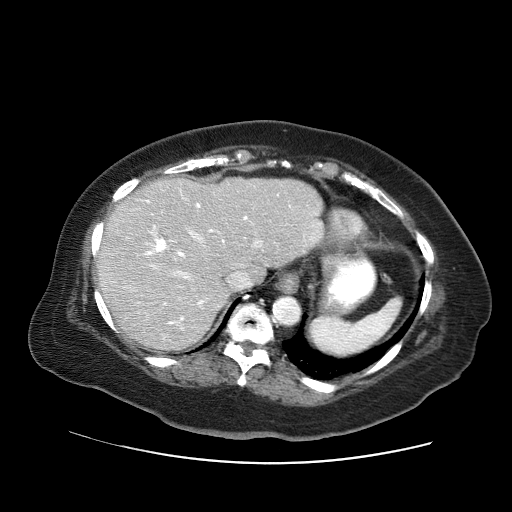
Contrast-enhanced abdominal CT (liver protocol), one axial slice. Position 46 of 71 along the scan axis. Reconstruction kernel STANDARD. Soft-tissue window (W 400 / L 40 HU). 2.5 mm slice thickness. 512 × 512 image matrix. From the clinical record (not read from this slice): diagnosis: hepatocellular carcinoma (patient treated with transarterial chemoembolisation; whether this scan precedes or follows treatment is not stated here); TNM stage (as recorded): Stage-II; Child-Pugh class: A; tumour differentiation: poorly differentiated; tumour nodularity: multinodular.
Structures marked on this image (semi-automatically segmented with operator editing):
- liver parenchyma outside the tumour (the mass and vessels are separate outlines, so this box may not span the whole liver): box from (x=96, y=178) to (x=324, y=352) px
- liver vessels: (x=138, y=190)–(x=321, y=340)